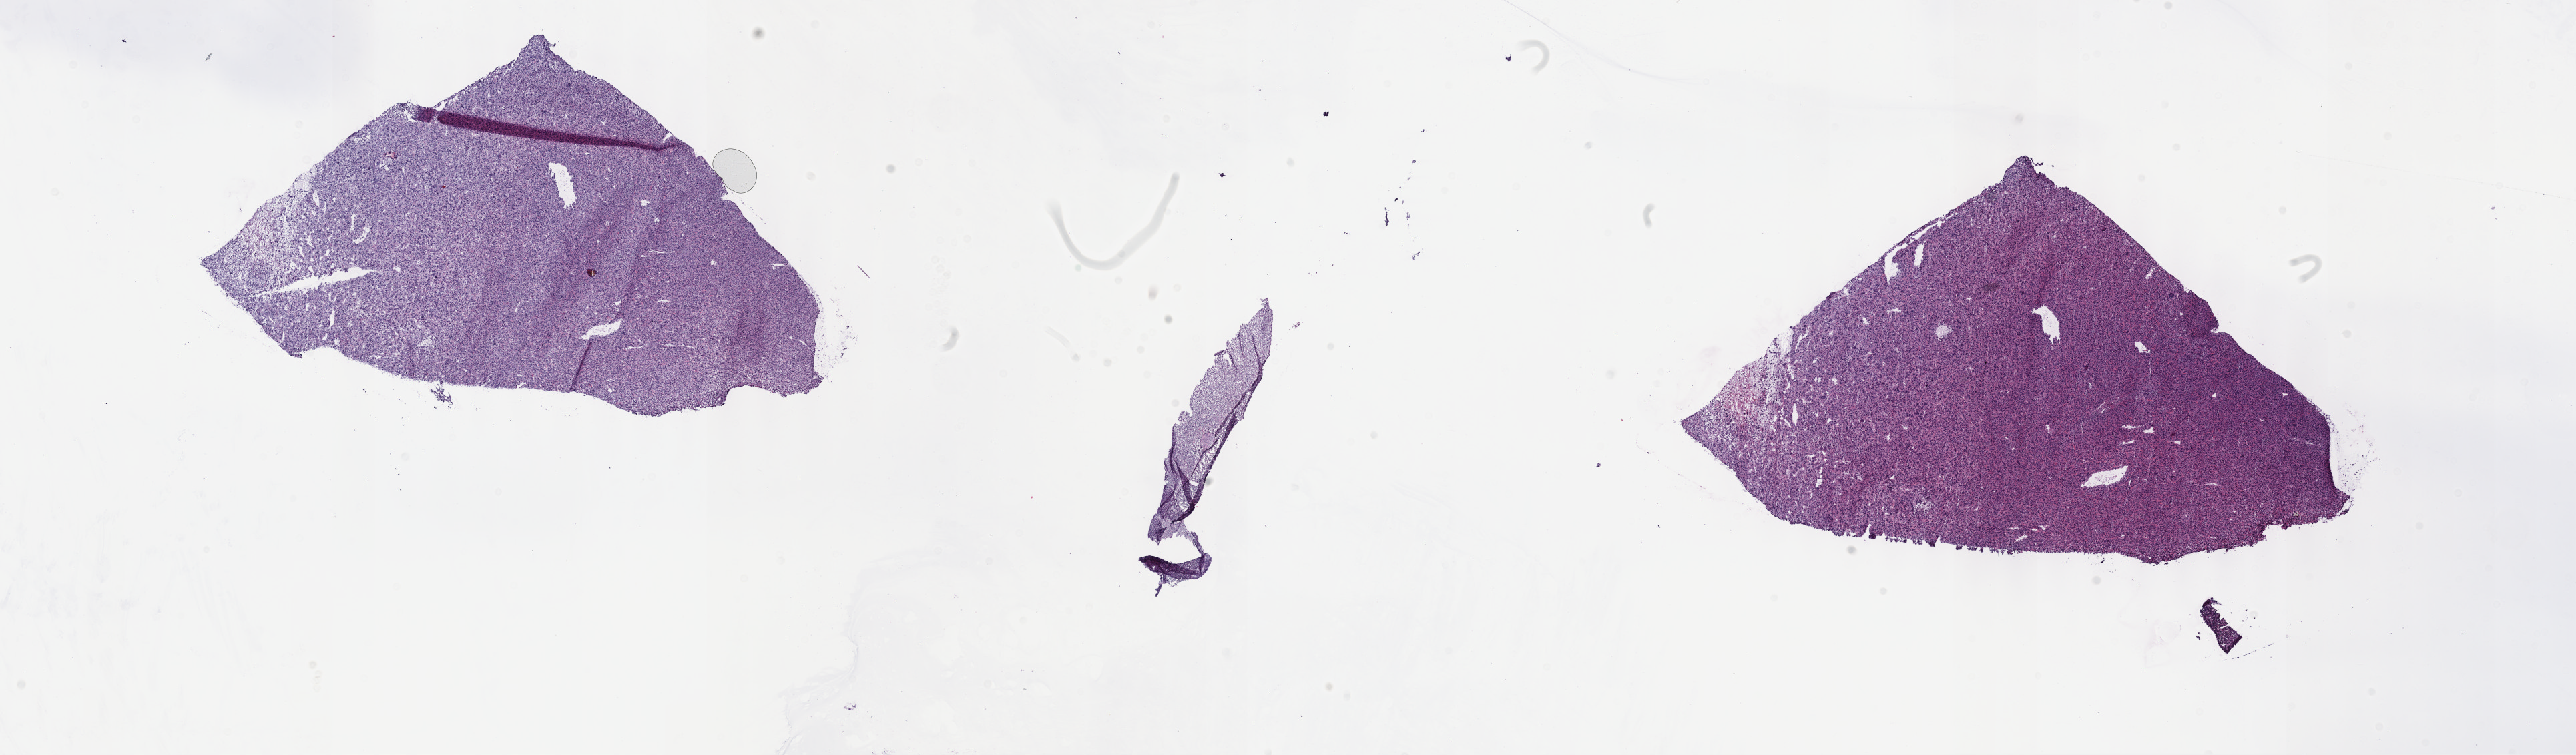
Hematoxylin and eosin (H&E) stained whole-slide image — low-resolution overview of the scanned area, about 31.2 x 9.1 mm (from a 40x scan). Frozen section from the top of the tissue portion. Connective, subcutaneous and other soft tissues, primary tumour sample. Patient: female, age at initial diagnosis 49 years.
Histologic diagnosis: Undifferentiated sarcoma (connective, subcutaneous and other soft tissues of thorax).